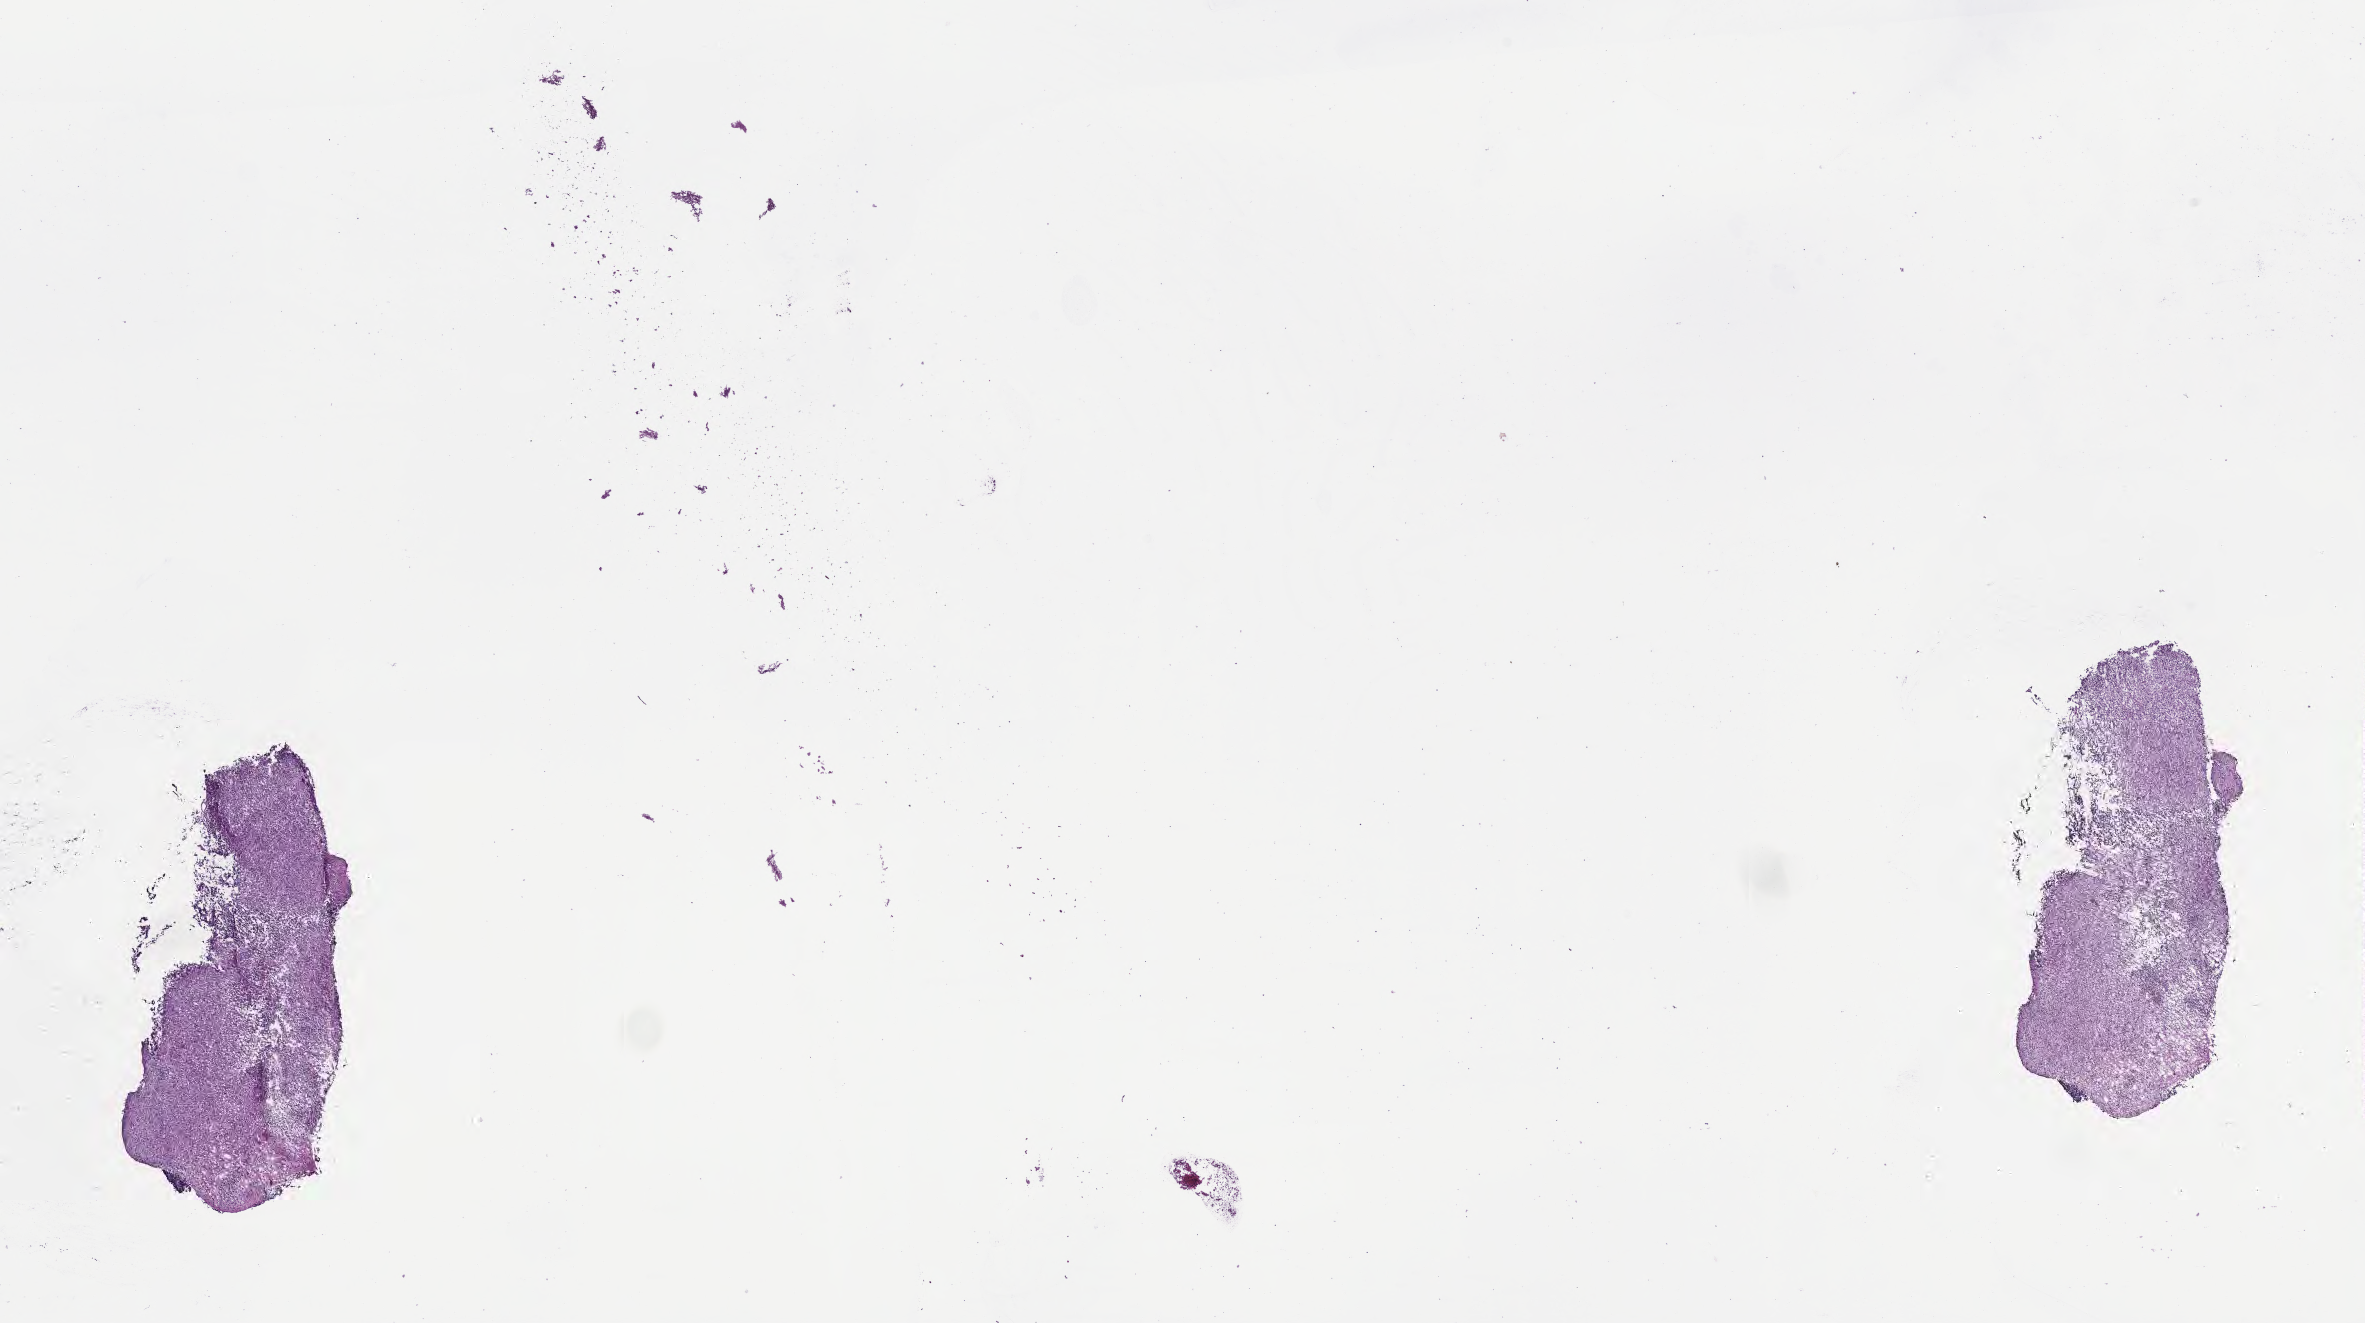
Whole-slide image, hematoxylin and eosin (H&E) stain of tumor tissue from the brain — a low-resolution overview of the entire scanned area, about 19.1 x 10.7 mm; frozen section (OCT-embedded). Female patient, age 66 months (5 years 6 months).
* diagnosis: Medulloblastoma, NOS